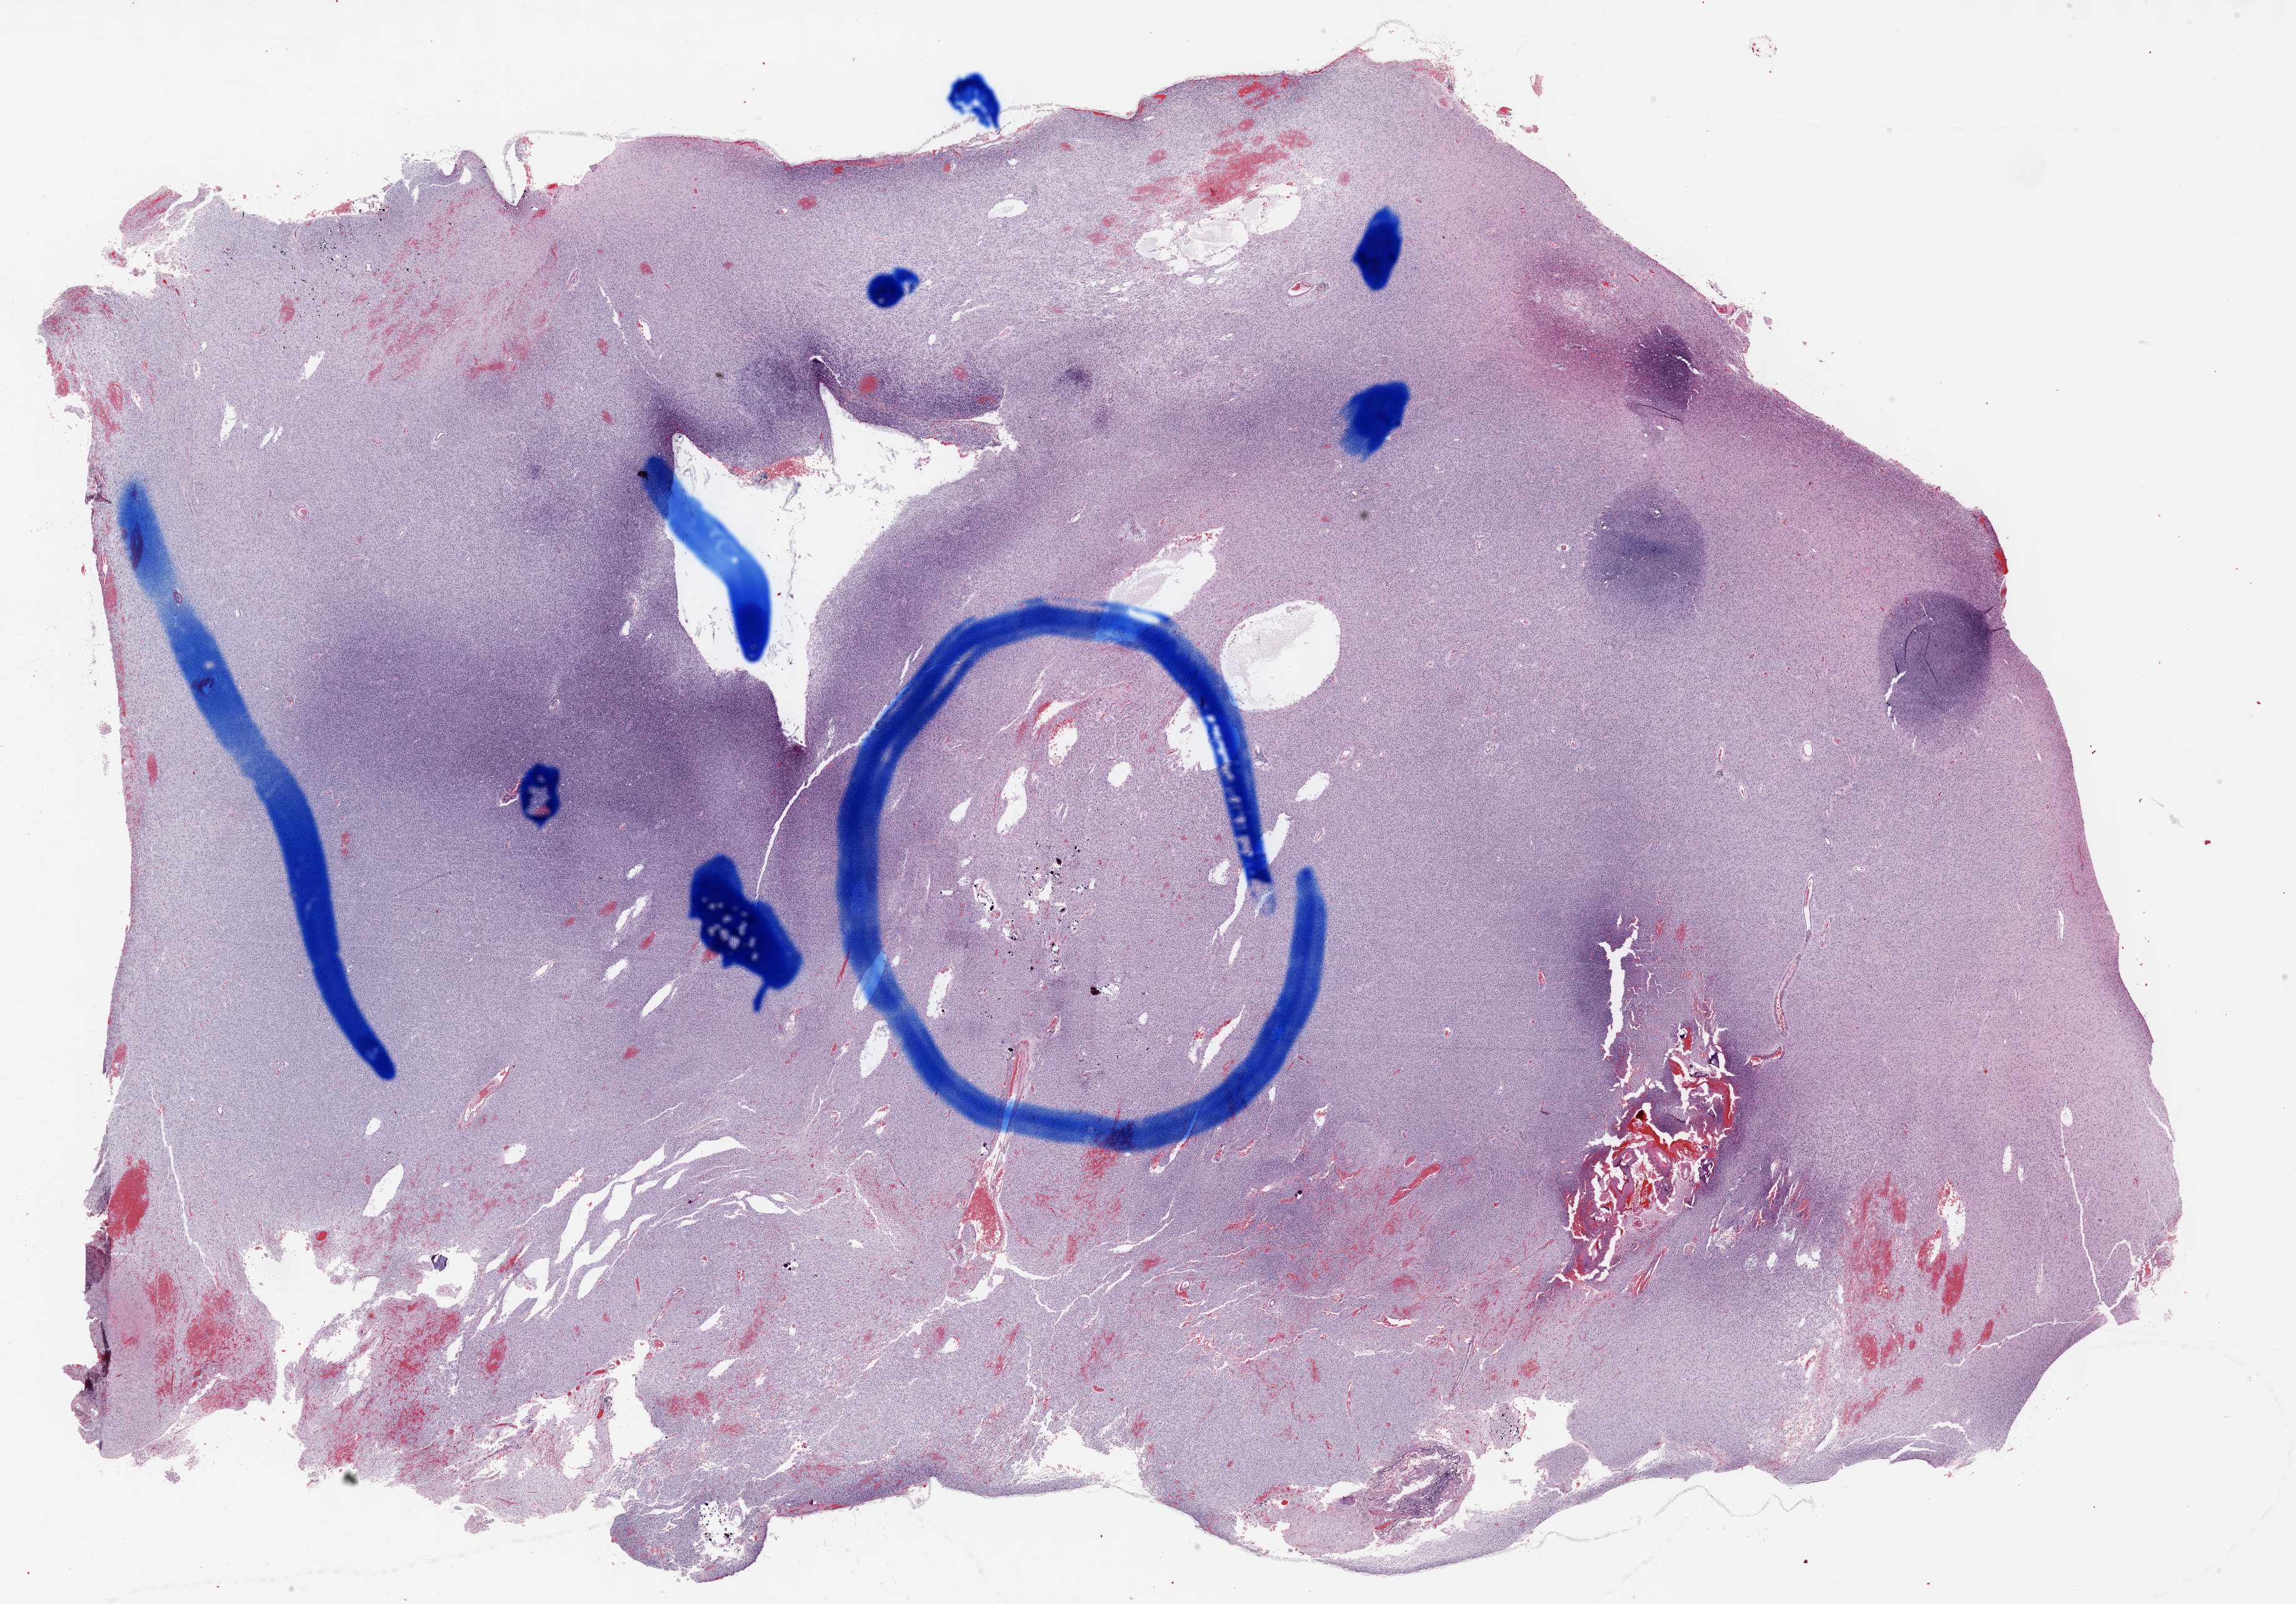
H&E-stained whole-slide image, a low-resolution overview of the entire scanned area, about 29.7 x 20.7 mm (acquisition: 40x scan), FFPE section, primary tumour sample from the brain. Male patient; age at initial diagnosis 26 years. Histologic grade: G3 (poorly differentiated).
* diagnosis: Mixed glioma (cerebrum)